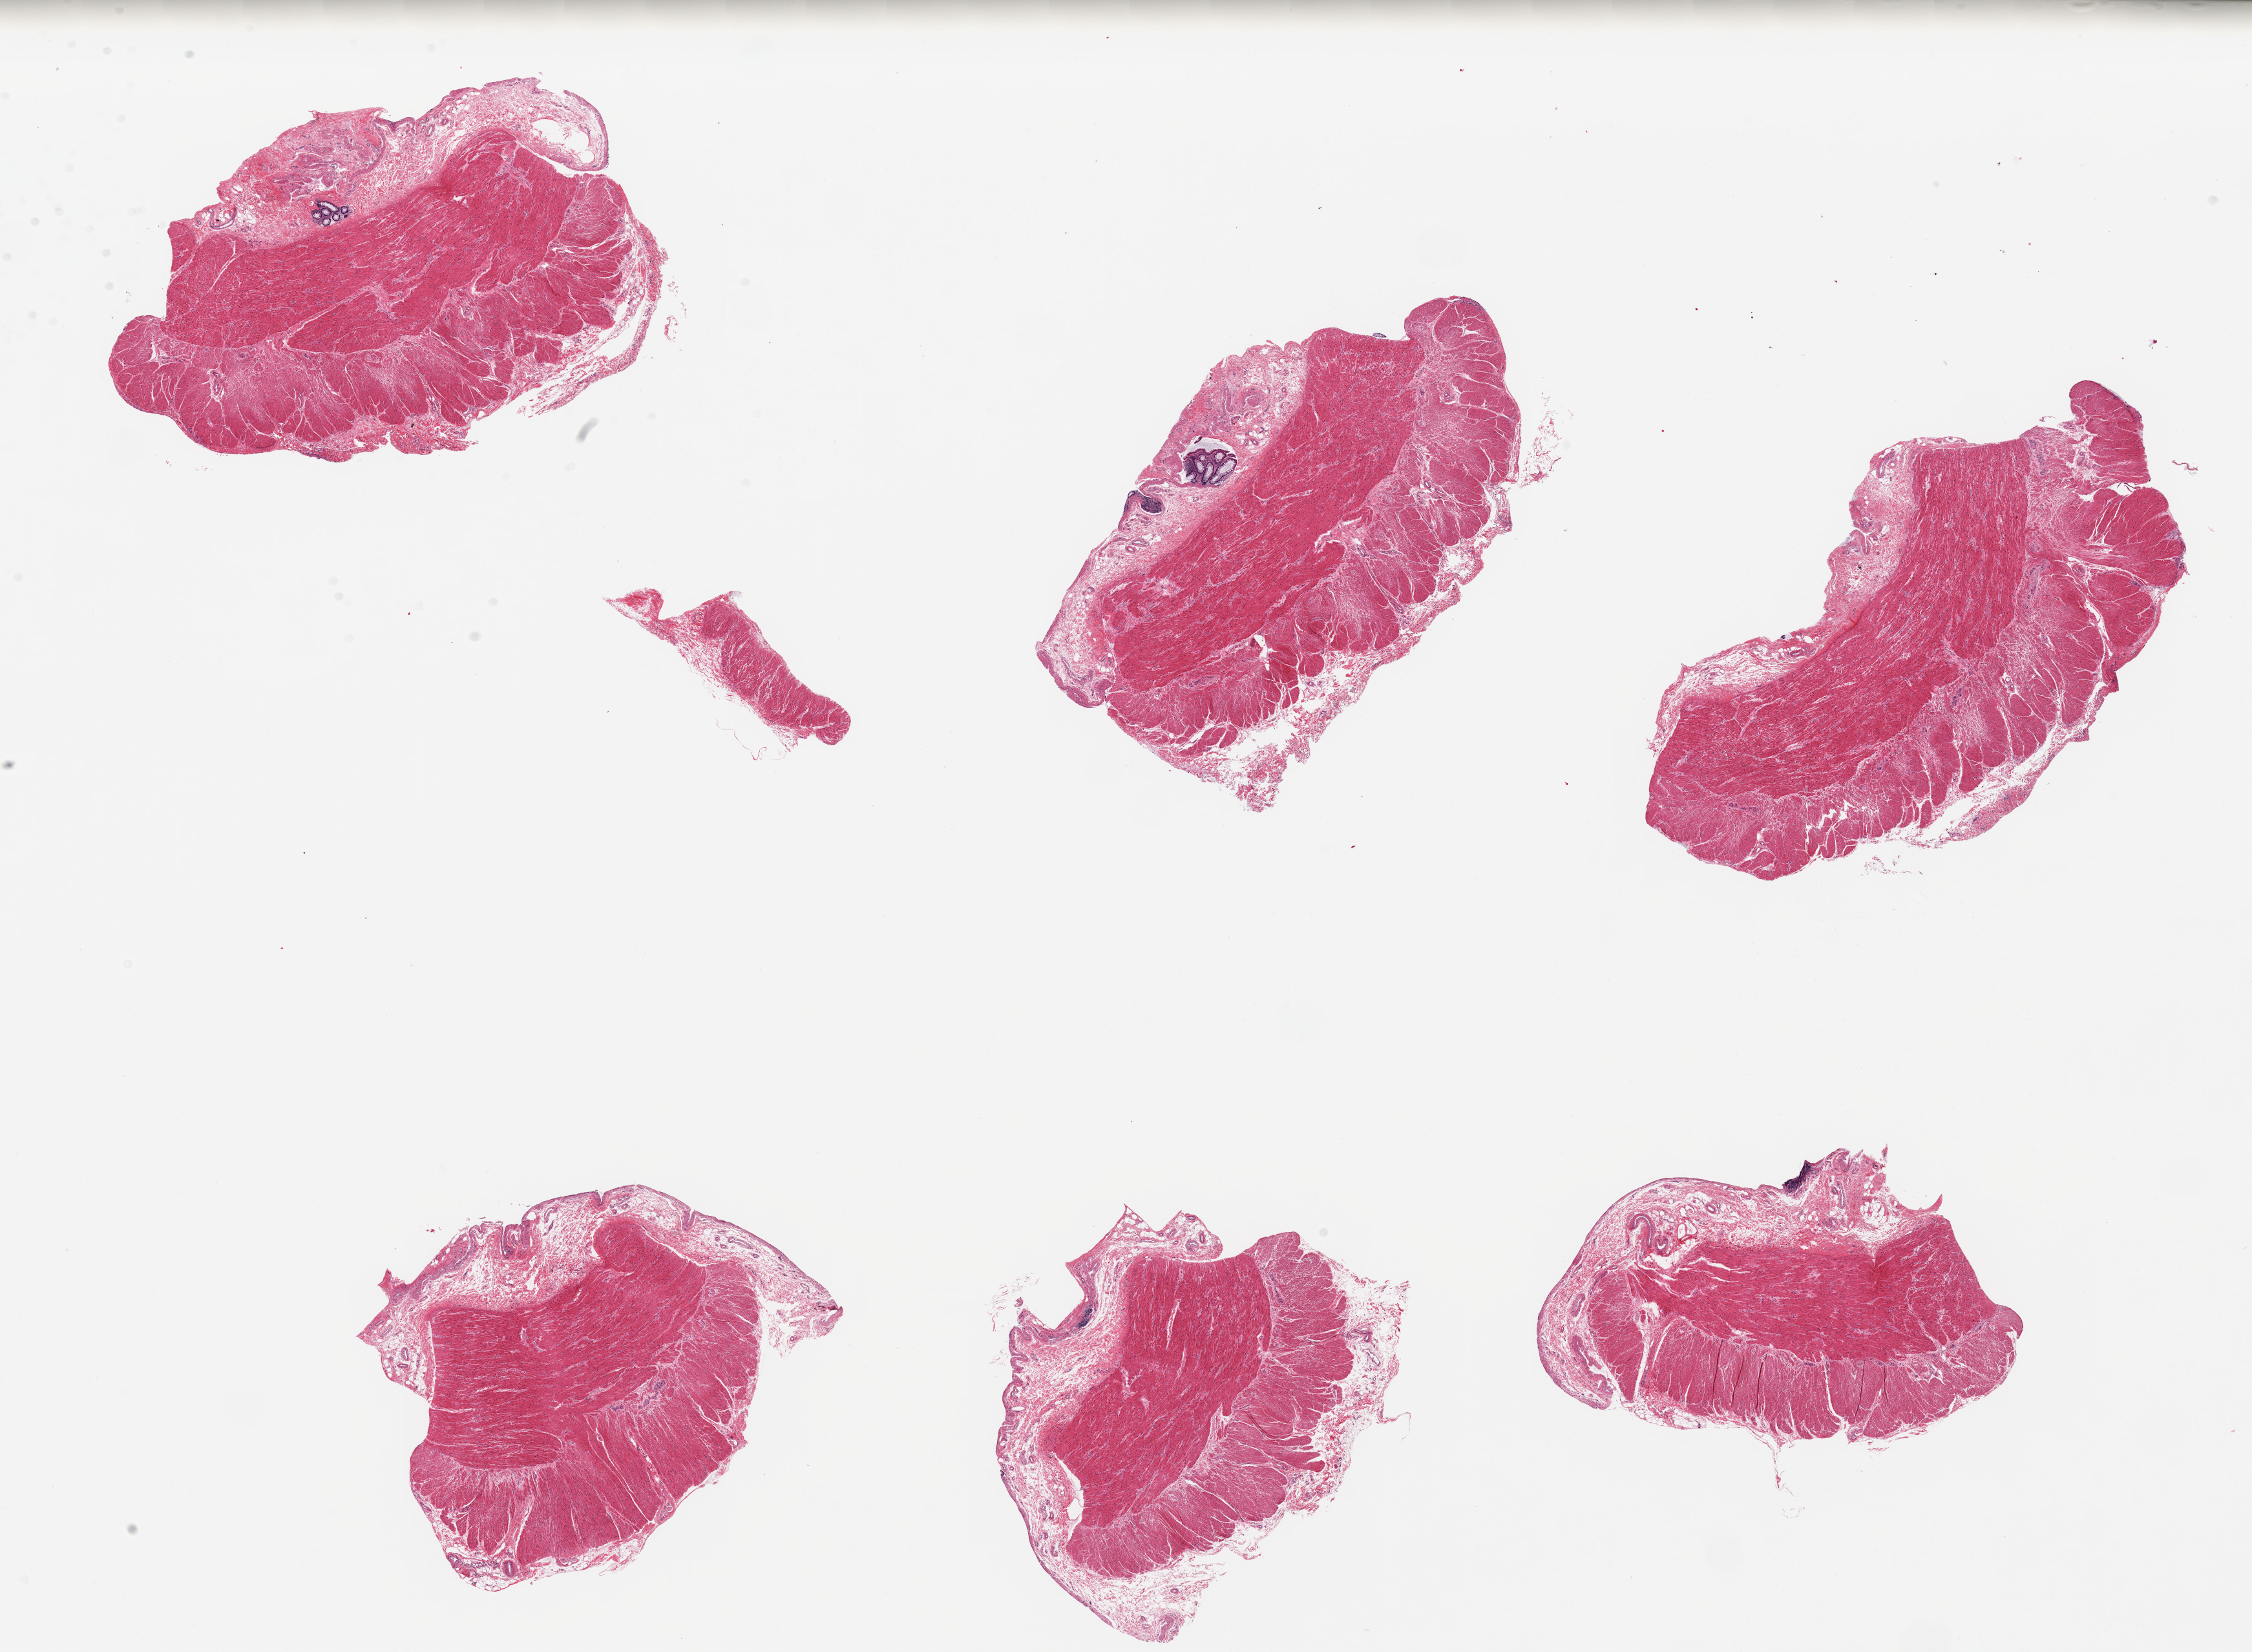
Digitized haematoxylin and eosin-stained section, shown as a low-resolution overview of the whole scanned area (about 27.6 x 20.2 mm, slide scanned at 20x). PAXgene-fixed paraffin-embedded (PFPE) section. Sampled site (target tissue): sigmoid colon. Tissue donor sample. Donor: female.
Review note (as recorded): 6 pieces; 2 small mucosal foci (not target).